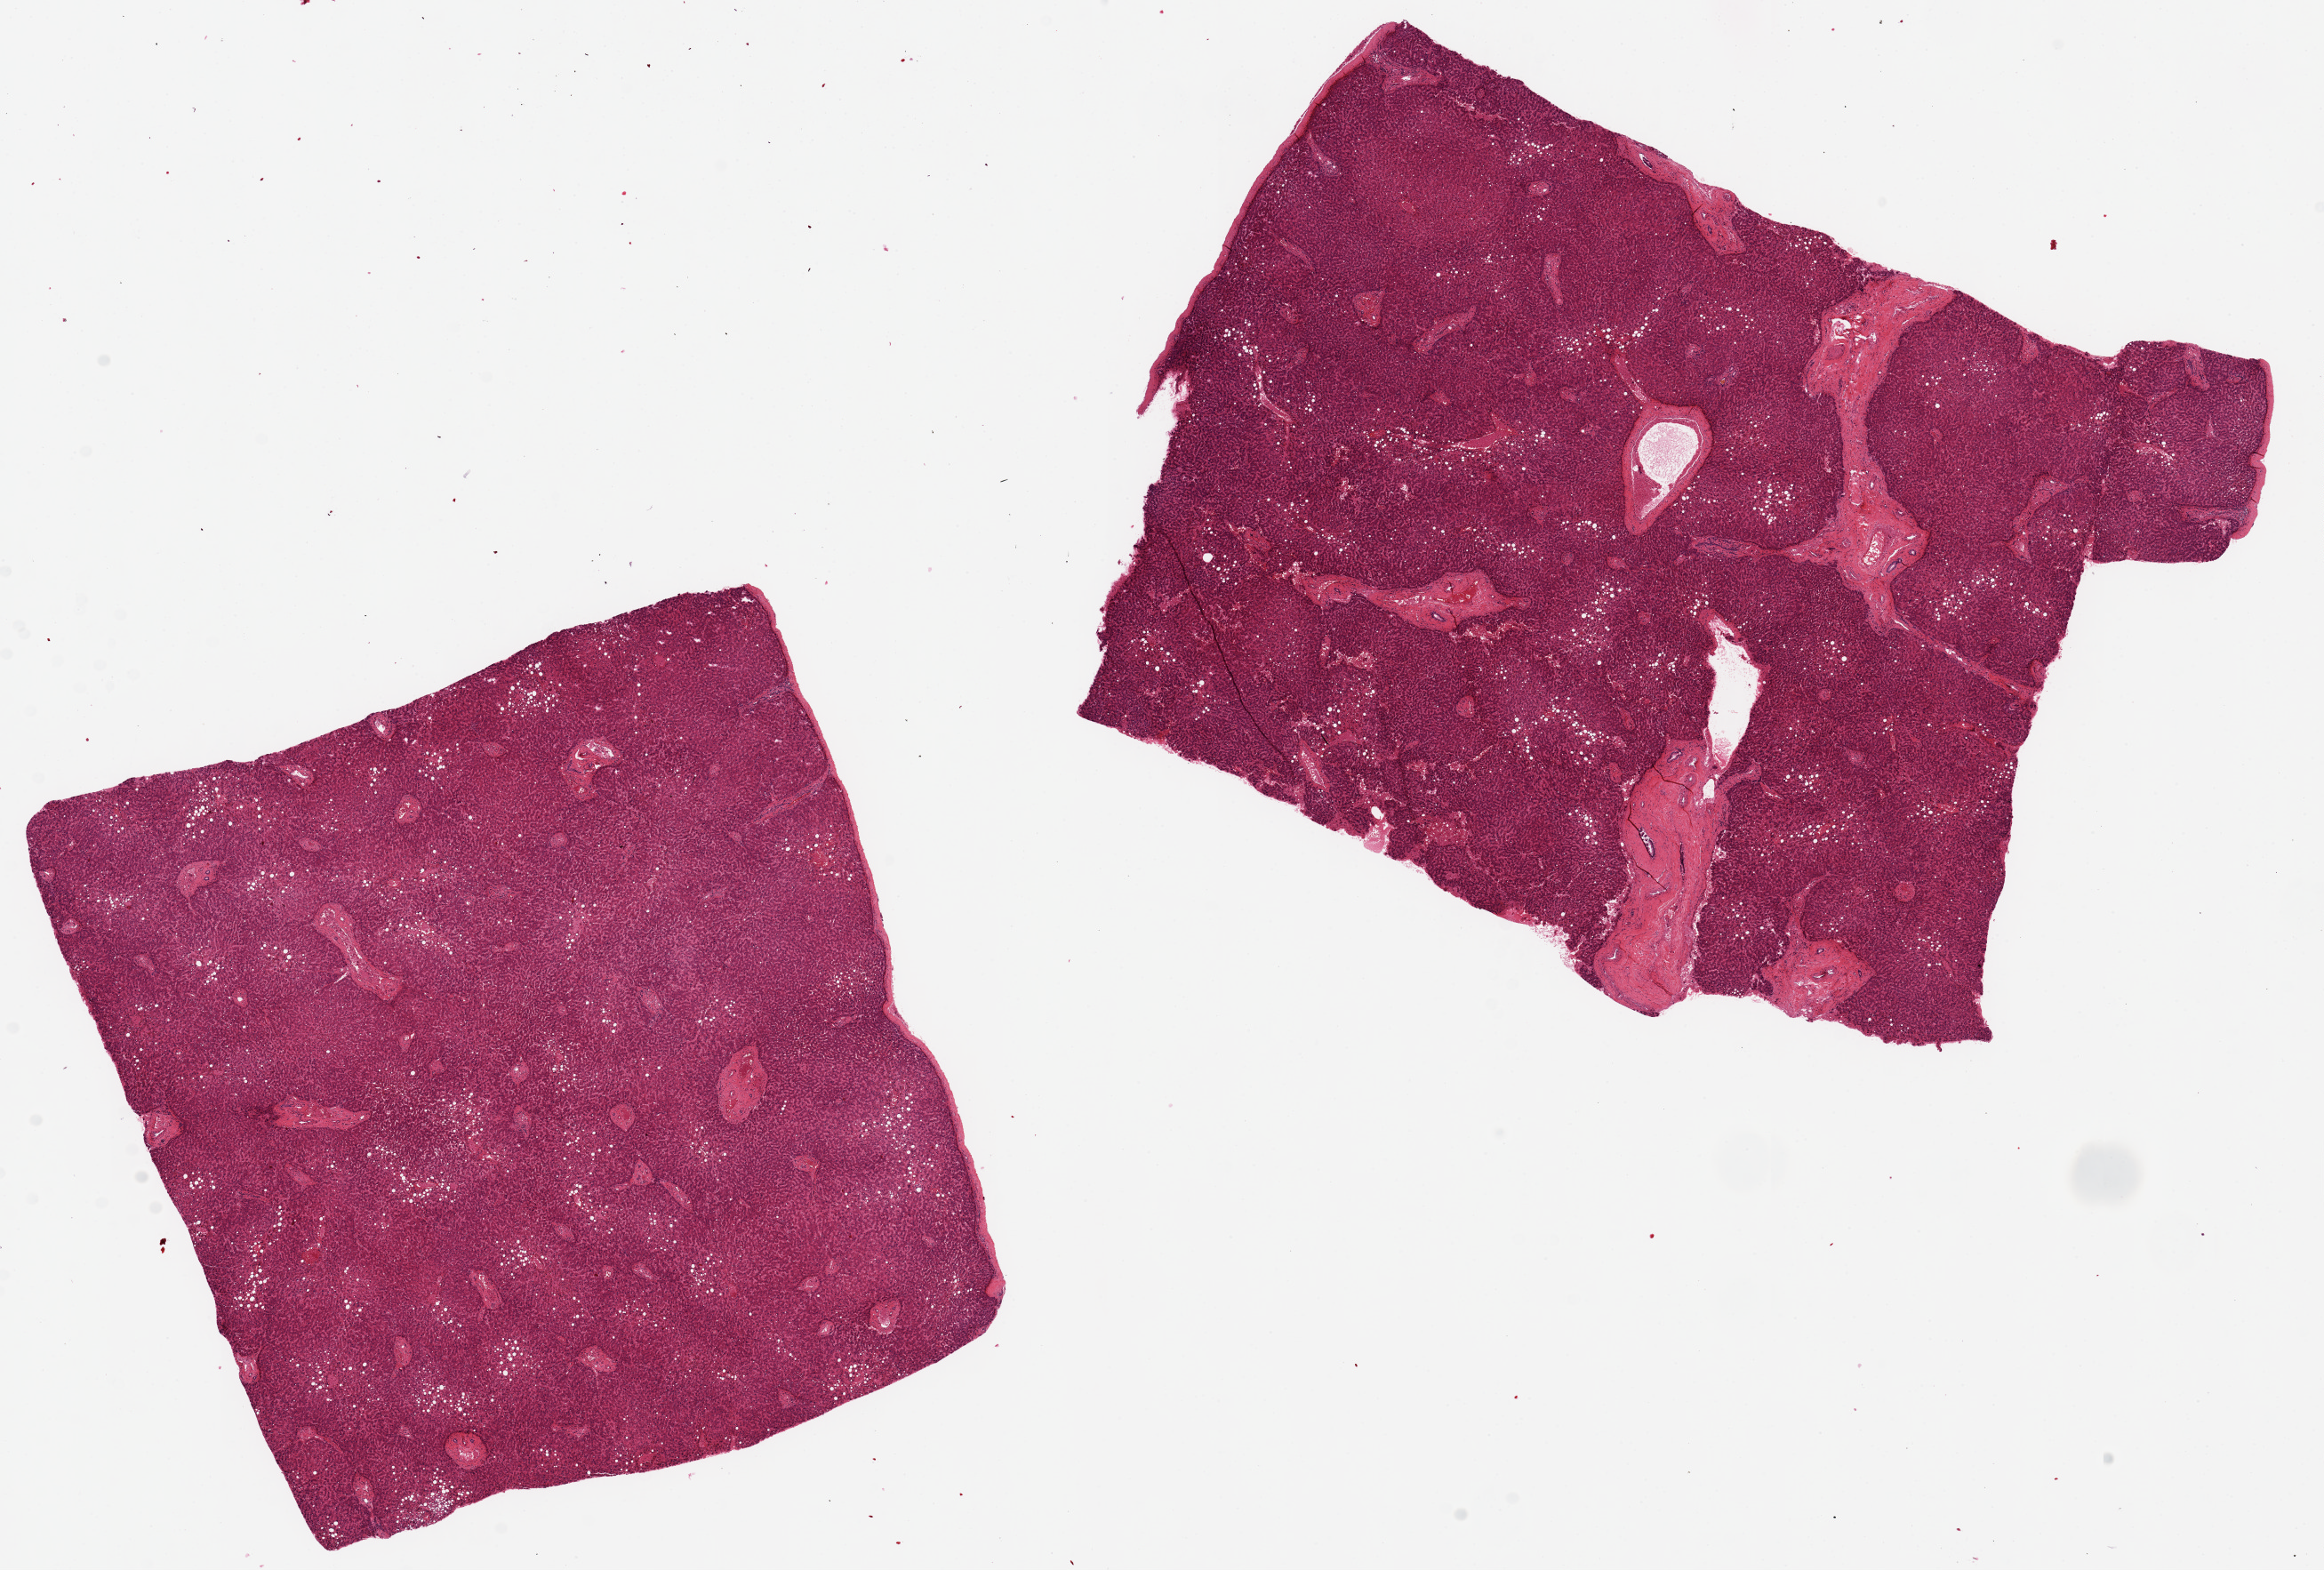
H&E whole-slide image, brightfield, whole scanned area (about 20.7 x 14.0 mm) shown as a low-resolution overview. PAXgene-fixed, paraffin-embedded tissue. Section of liver (target tissue). Tissue donor sample. Donor: male.
Pathologist's review note for this sample: 2 pieces ~7x7mm, 30% macrovesicular steatosis, moderate passive congestion.